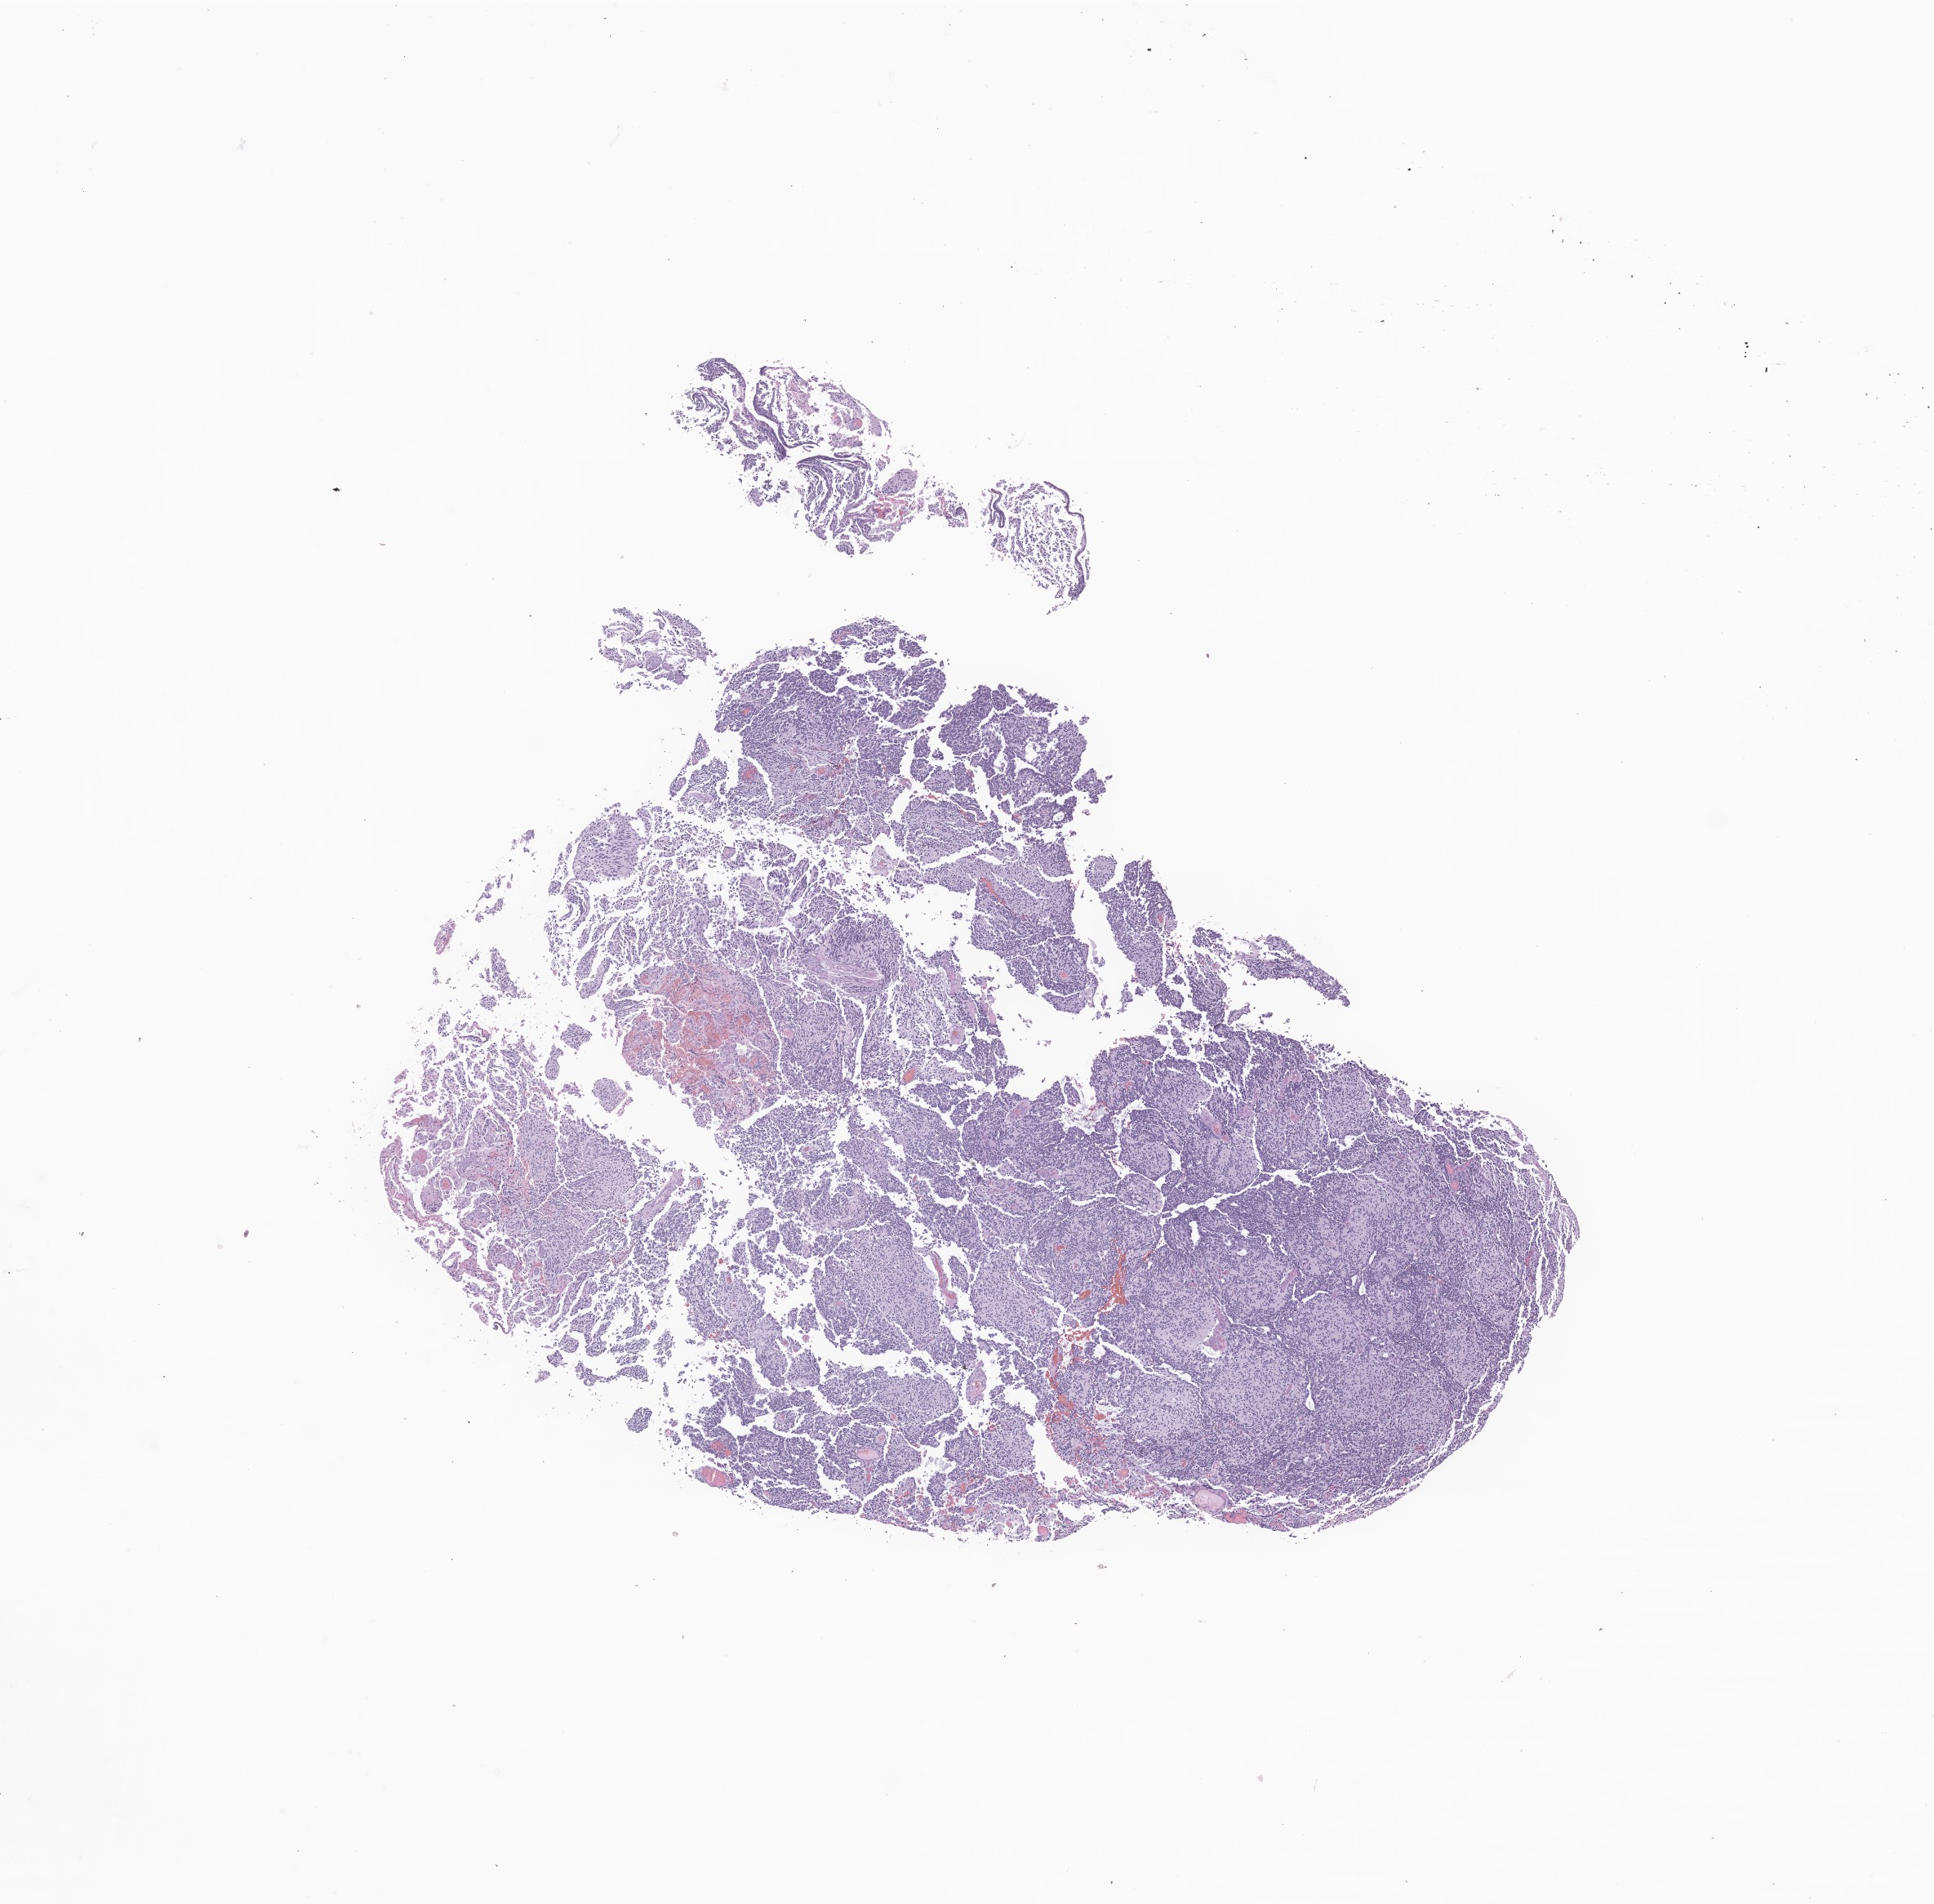
Whole-slide image, haematoxylin and eosin stain of tumor tissue from the brain — shown as a low-resolution overview of the whole scanned area (about 10.0 x 9.8 mm). Formalin-fixed paraffin-embedded section. Patient male; age 83 months.
Diagnosis (ICD-O-3 morphology term): Medulloblastoma, NOS.